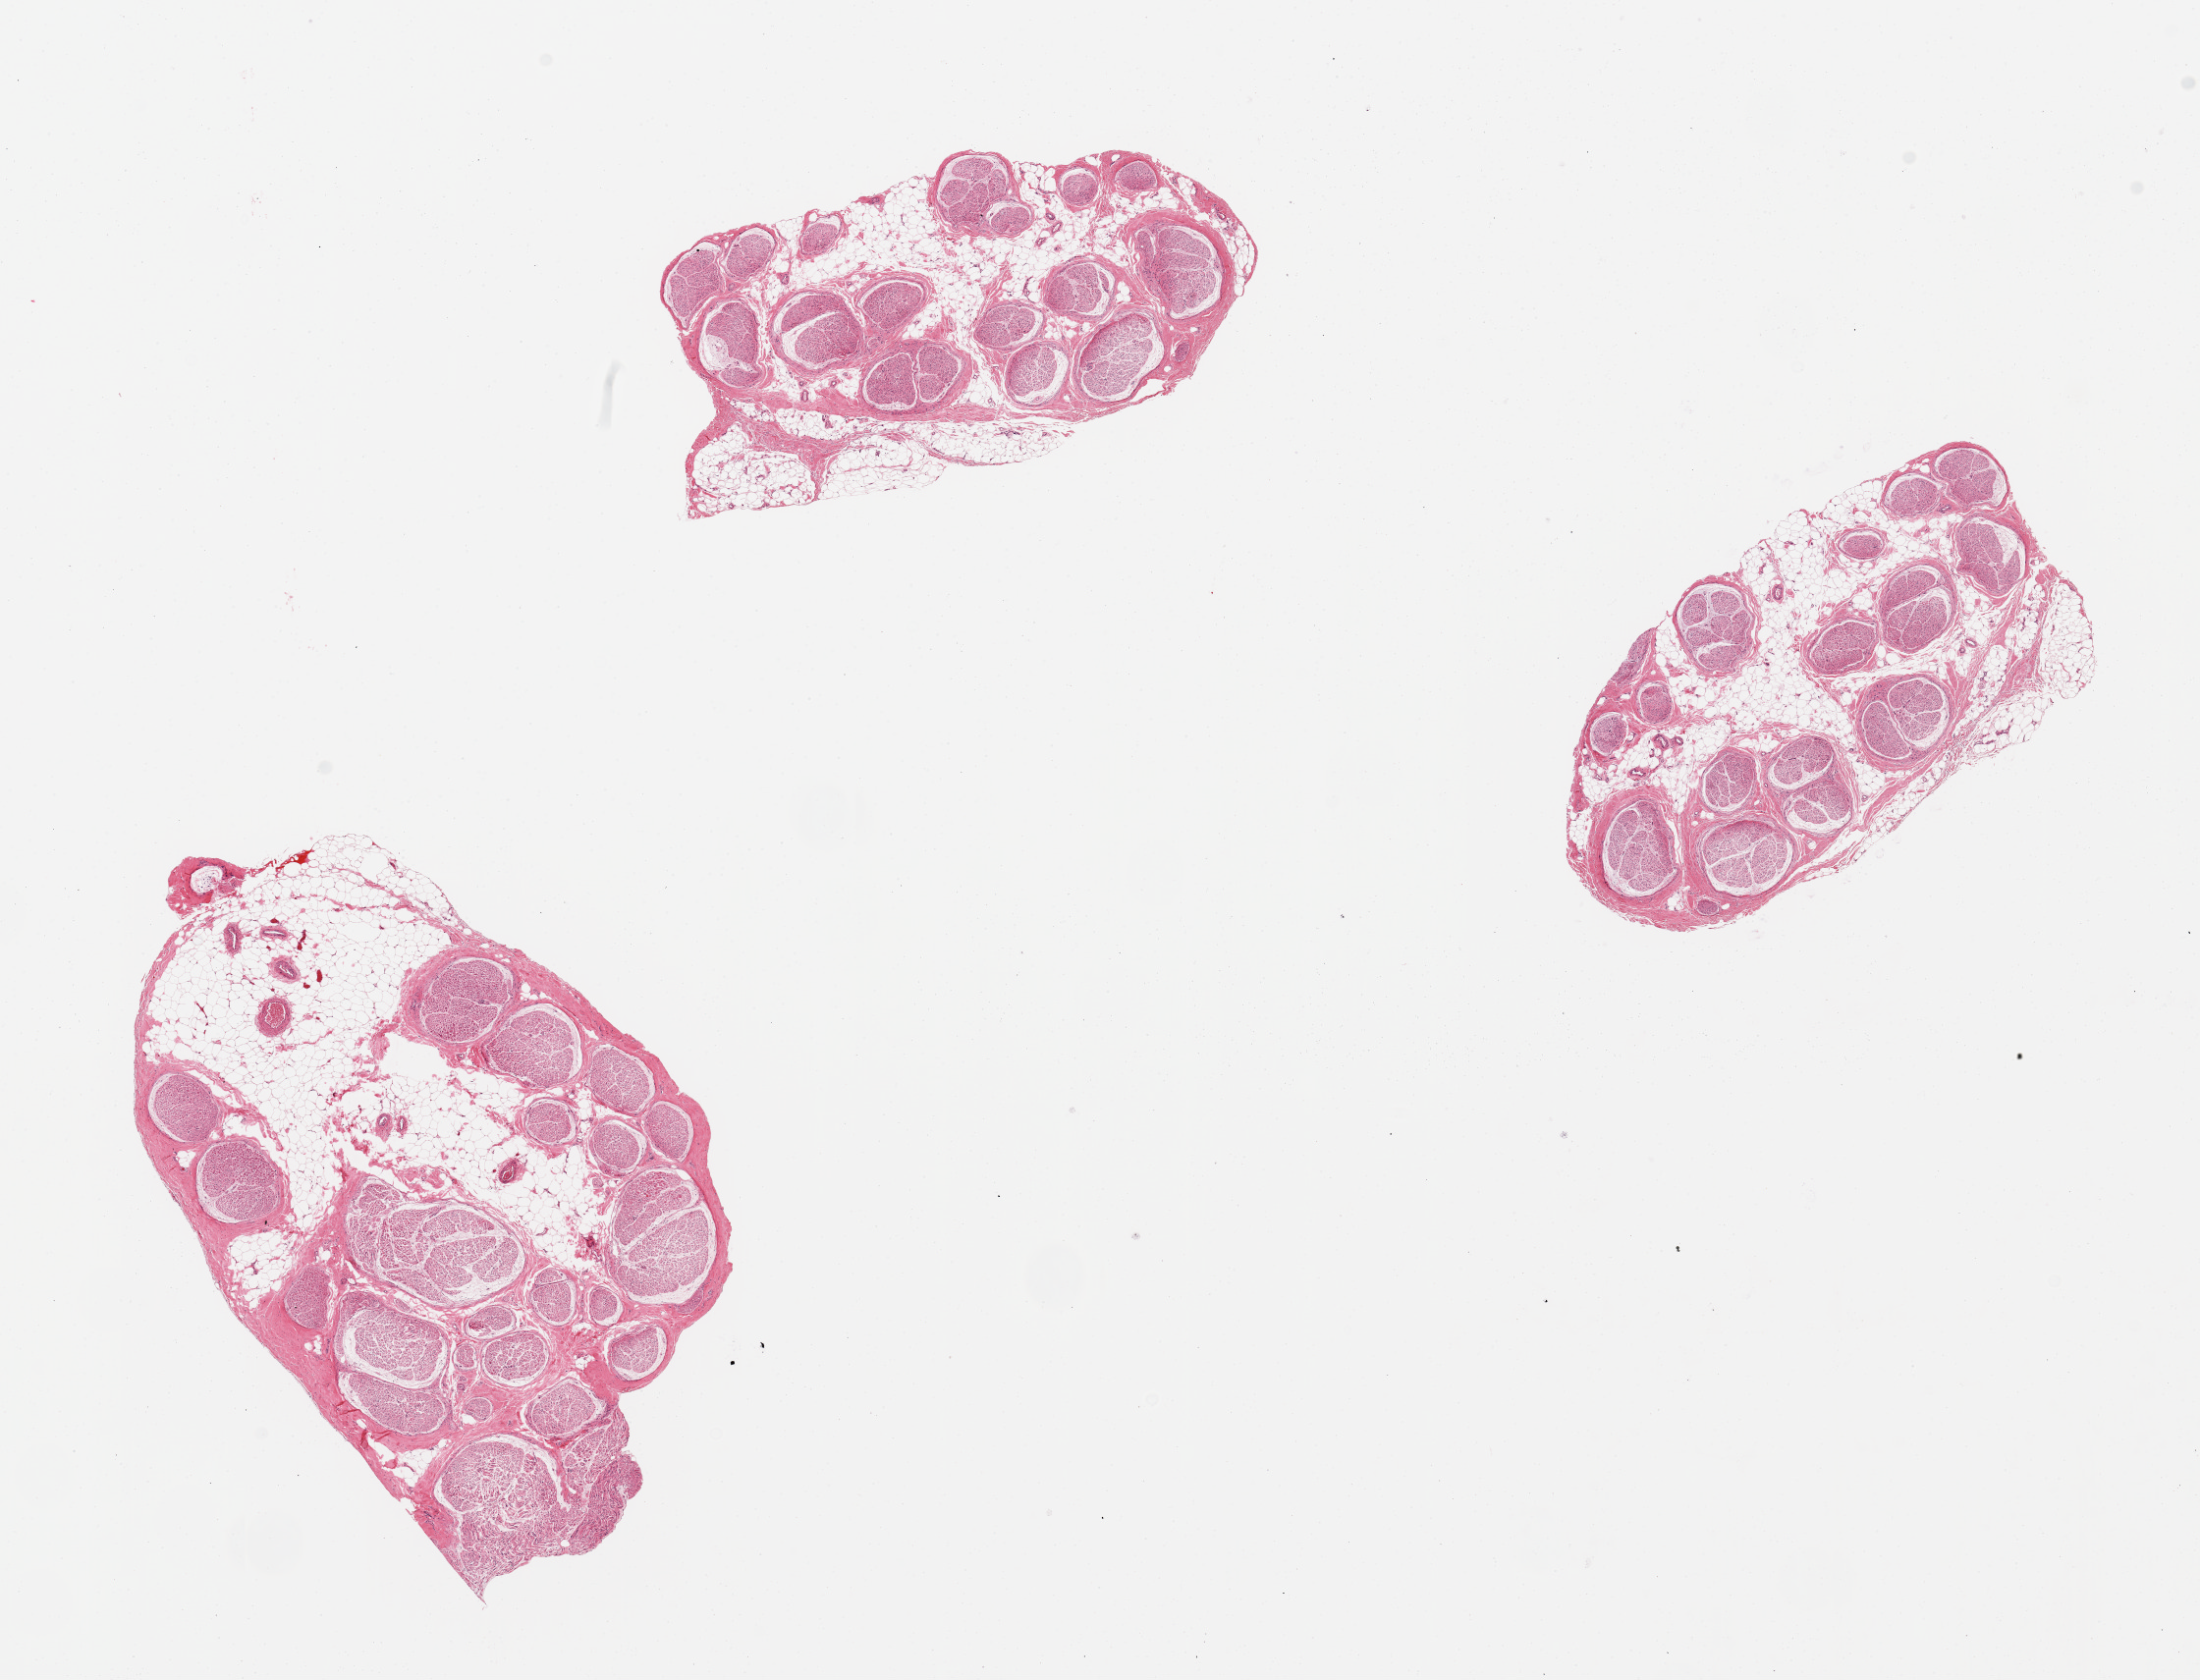
Digitized H&E-stained section — whole scanned area (about 17.7 x 13.5 mm, acquisition: 20x scan) shown as a low-resolution overview; PAXgene-fixed, paraffin-embedded tissue; section of tibial nerve (target tissue); tissue donor sample.
Review note (as recorded): 3 pieces; 20 - 40% internal fat.